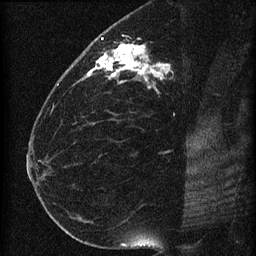
Breast MRI (dynamic contrast-enhanced), one sagittal slice; slice 33 of 60 in the series (ordered by position); dynamic contrast-enhanced series, image 2 of 4 at this slice position (ordered by acquisition); 1.5 T; TE 4.2 ms, TR 22.7 ms; 1.5 mm slice thickness; 256 × 256 image matrix, field of view 180 × 180 mm. Patient: female, 35 years. Case-level facts recorded for this patient, not image findings: setting: breast cancer imaged before/during neoadjuvant chemotherapy; receptor status: HR-positive, HER2-negative.
Annotated regions visible in this slice (semi-automatically segmented with operator editing):
- analysis volume of interest (the breast-tissue region the enhancement analysis was run in; not a lesion): bounding box <69,27,199,112> (left, top, right, bottom; pixels)
- tumour enhancement mask (voxels above the 90 % enhancement threshold inside the analysis volume of interest): <85,37,169,83>